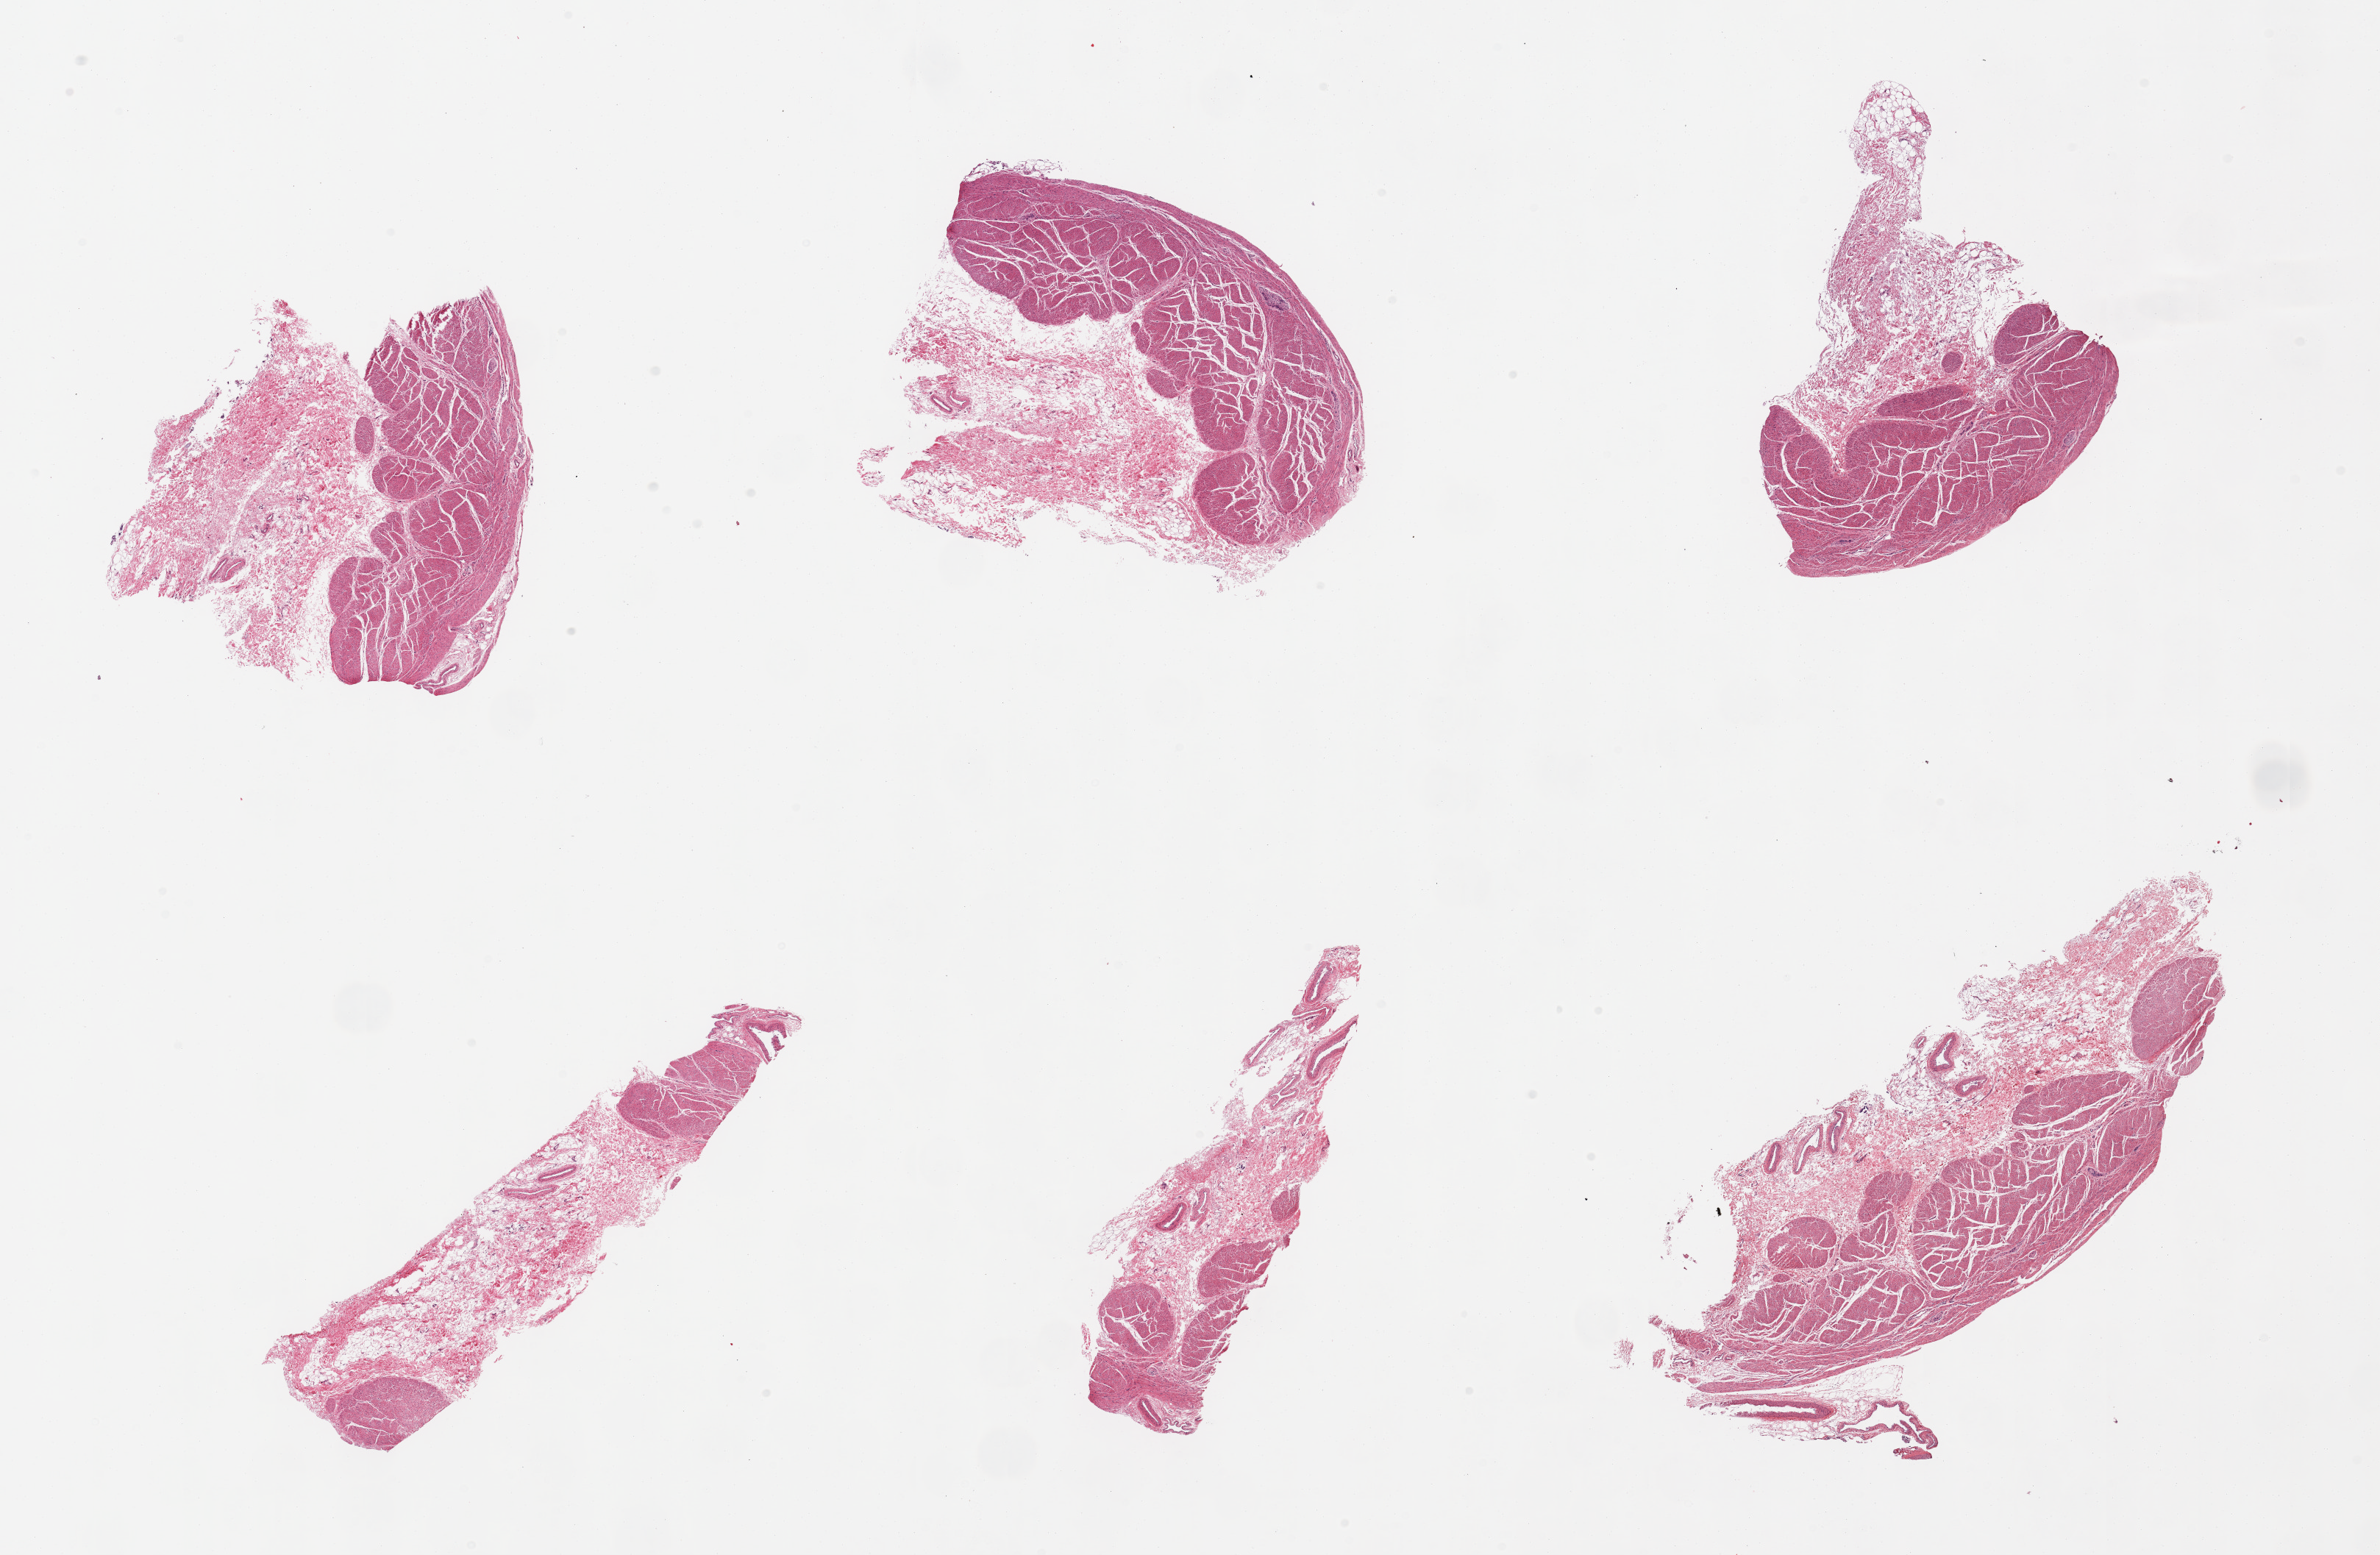
Haematoxylin and eosin whole-slide image, whole scanned area (about 25.6 x 16.7 mm) shown as a low-resolution overview, PAXgene-fixed paraffin-embedded (PFPE) section, sampled site (target tissue): gastroesophageal junction, tissue donor sample. Donor sex: male.
Pathologist's review note for this sample: 6 pieces; submucosal fibrous tissue occupies up to 50%.